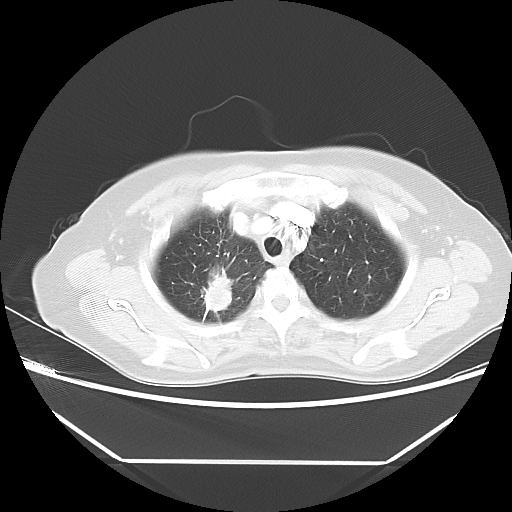
Chest CT, one axial slice; slice 41 of 48 in the series (ordered by position); 100 kVp; lung window (W 1500 / L -600 HU); 512 × 512 image matrix, field of view 360 × 360 mm. Female patient, age 65 years. From the clinical record (not read from this slice): clinical TNM (as recorded): T1c N1 M1.
Annotated regions visible in this slice (bounding box drawn by a radiologist):
- lung tumour (recorded histology: adenocarcinoma): box from (x=198, y=264) to (x=238, y=321) px